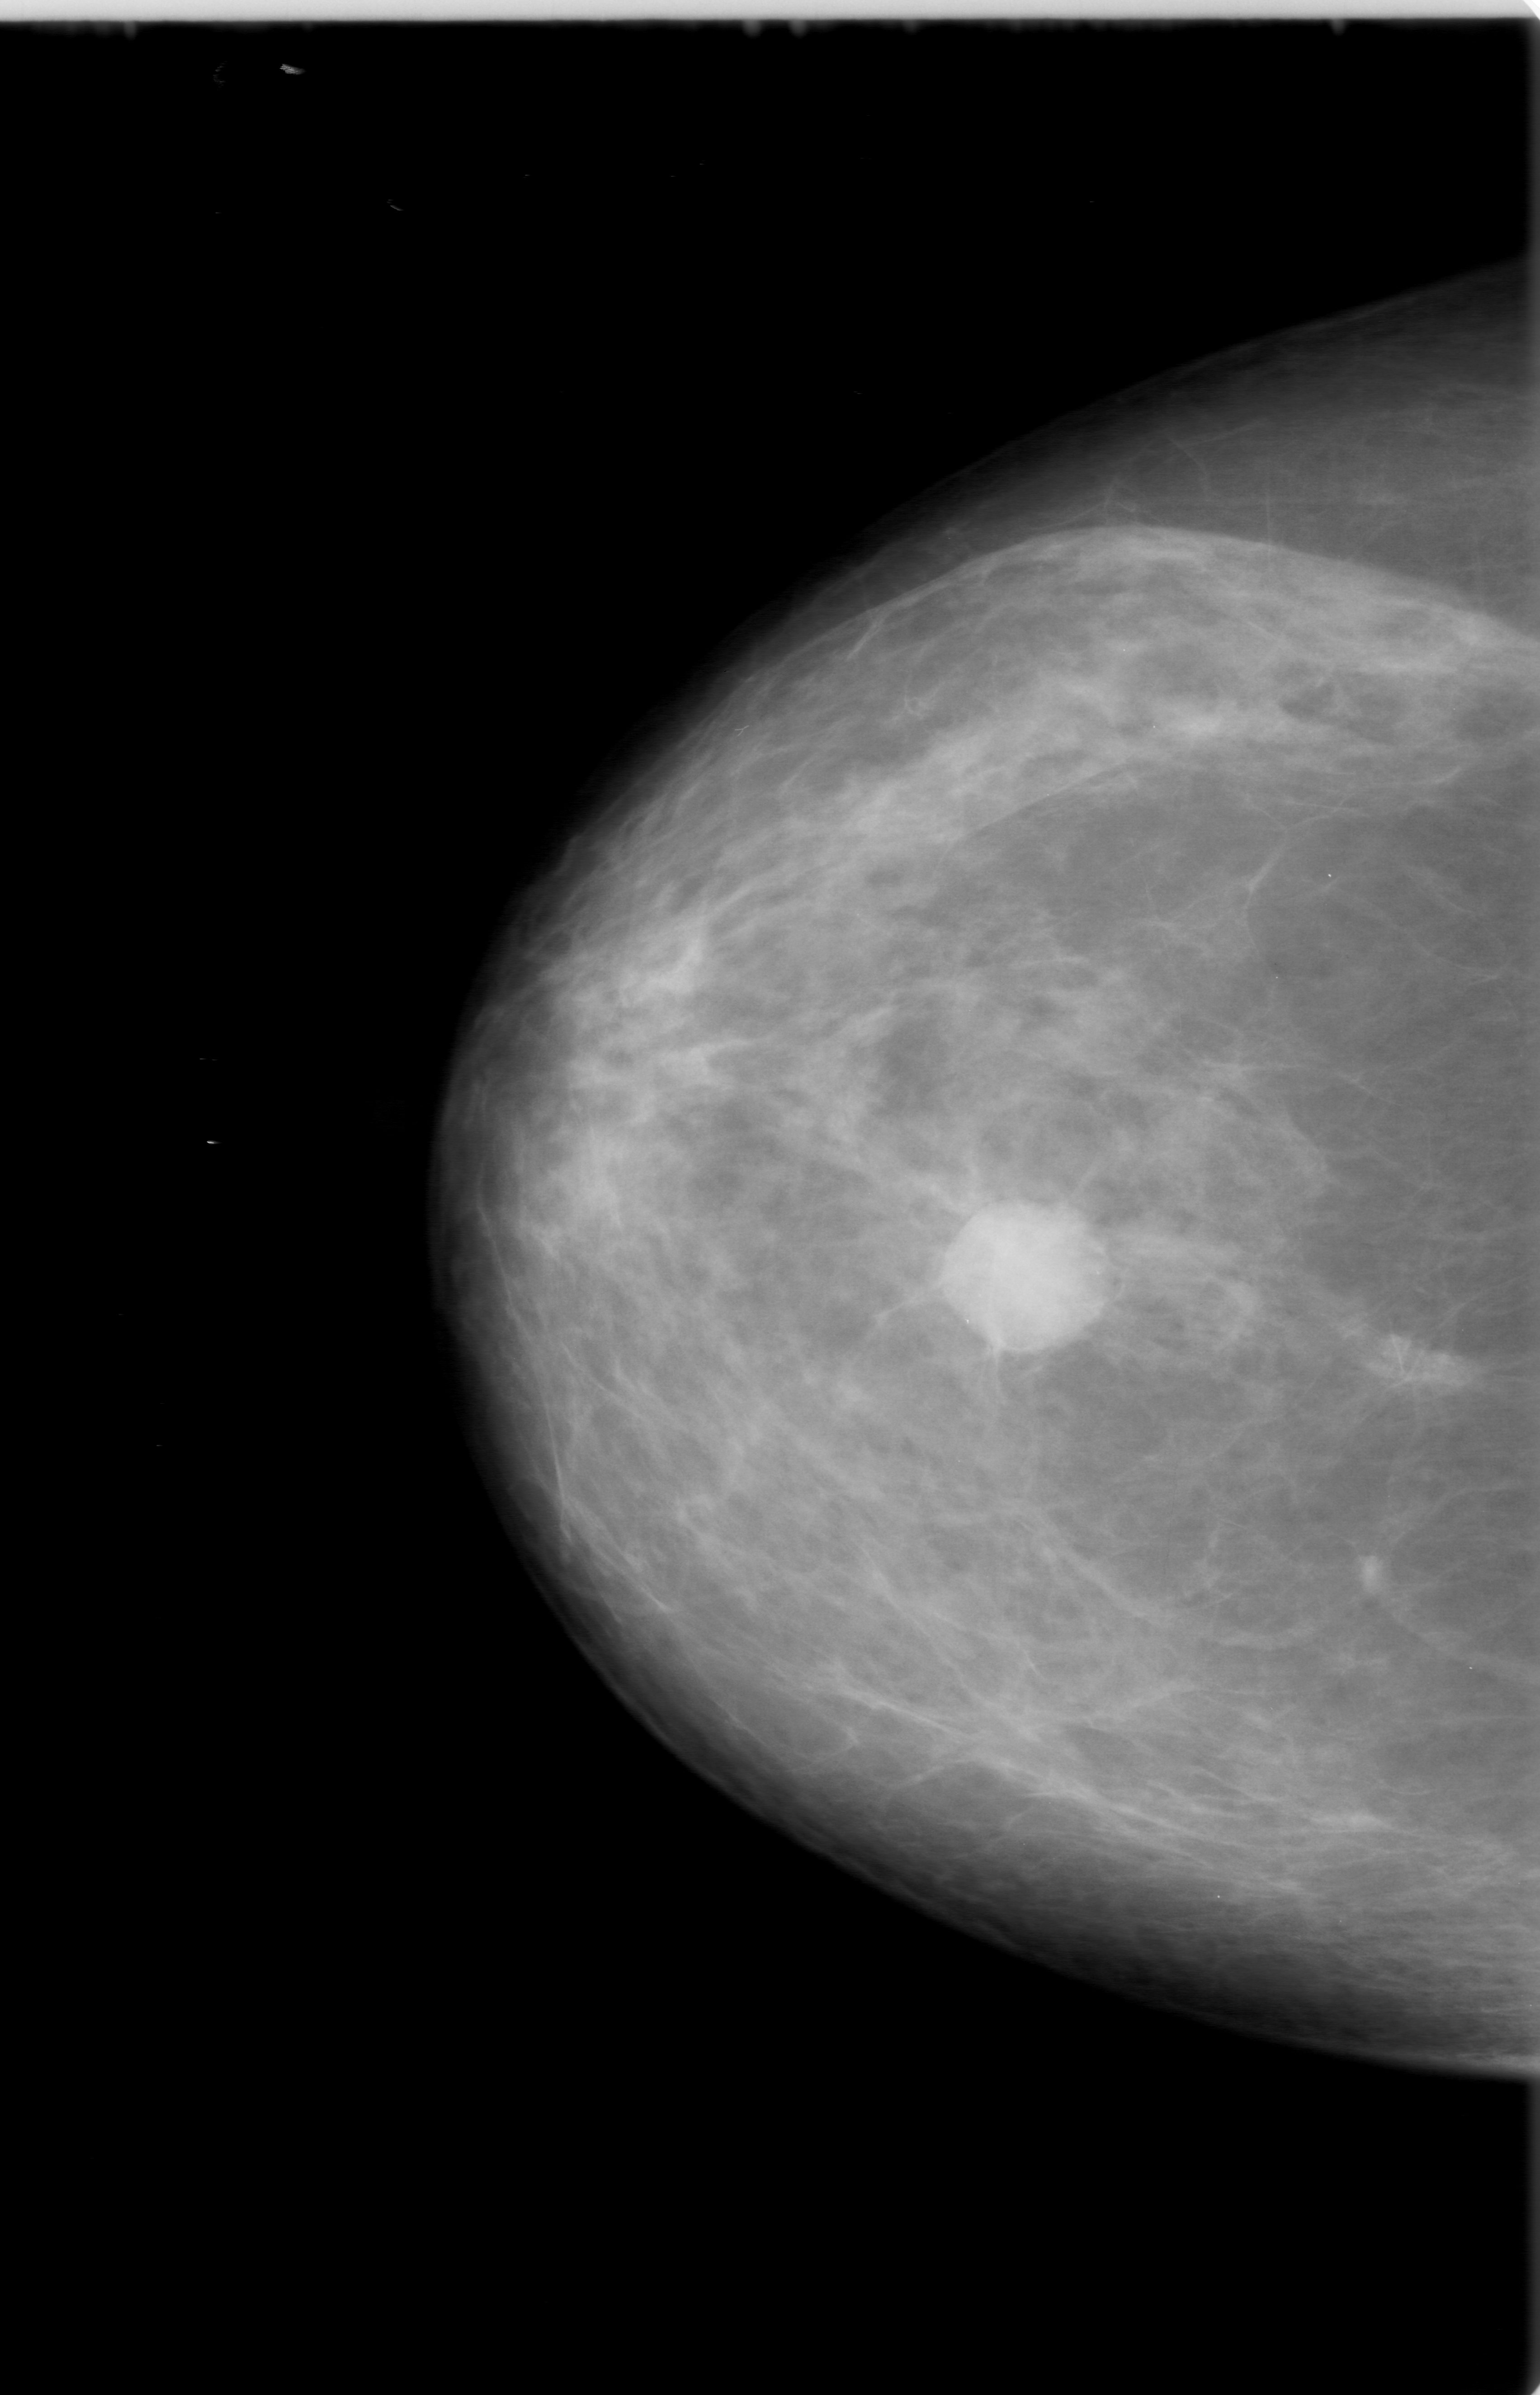
Mammogram (digitized film), right breast, CC view, BI-RADS breast density category 2 (scale 1–4).
Mass, shape round, margins spiculated; BI-RADS assessment category 3; pathology result (as recorded, not read from the image): malignant.